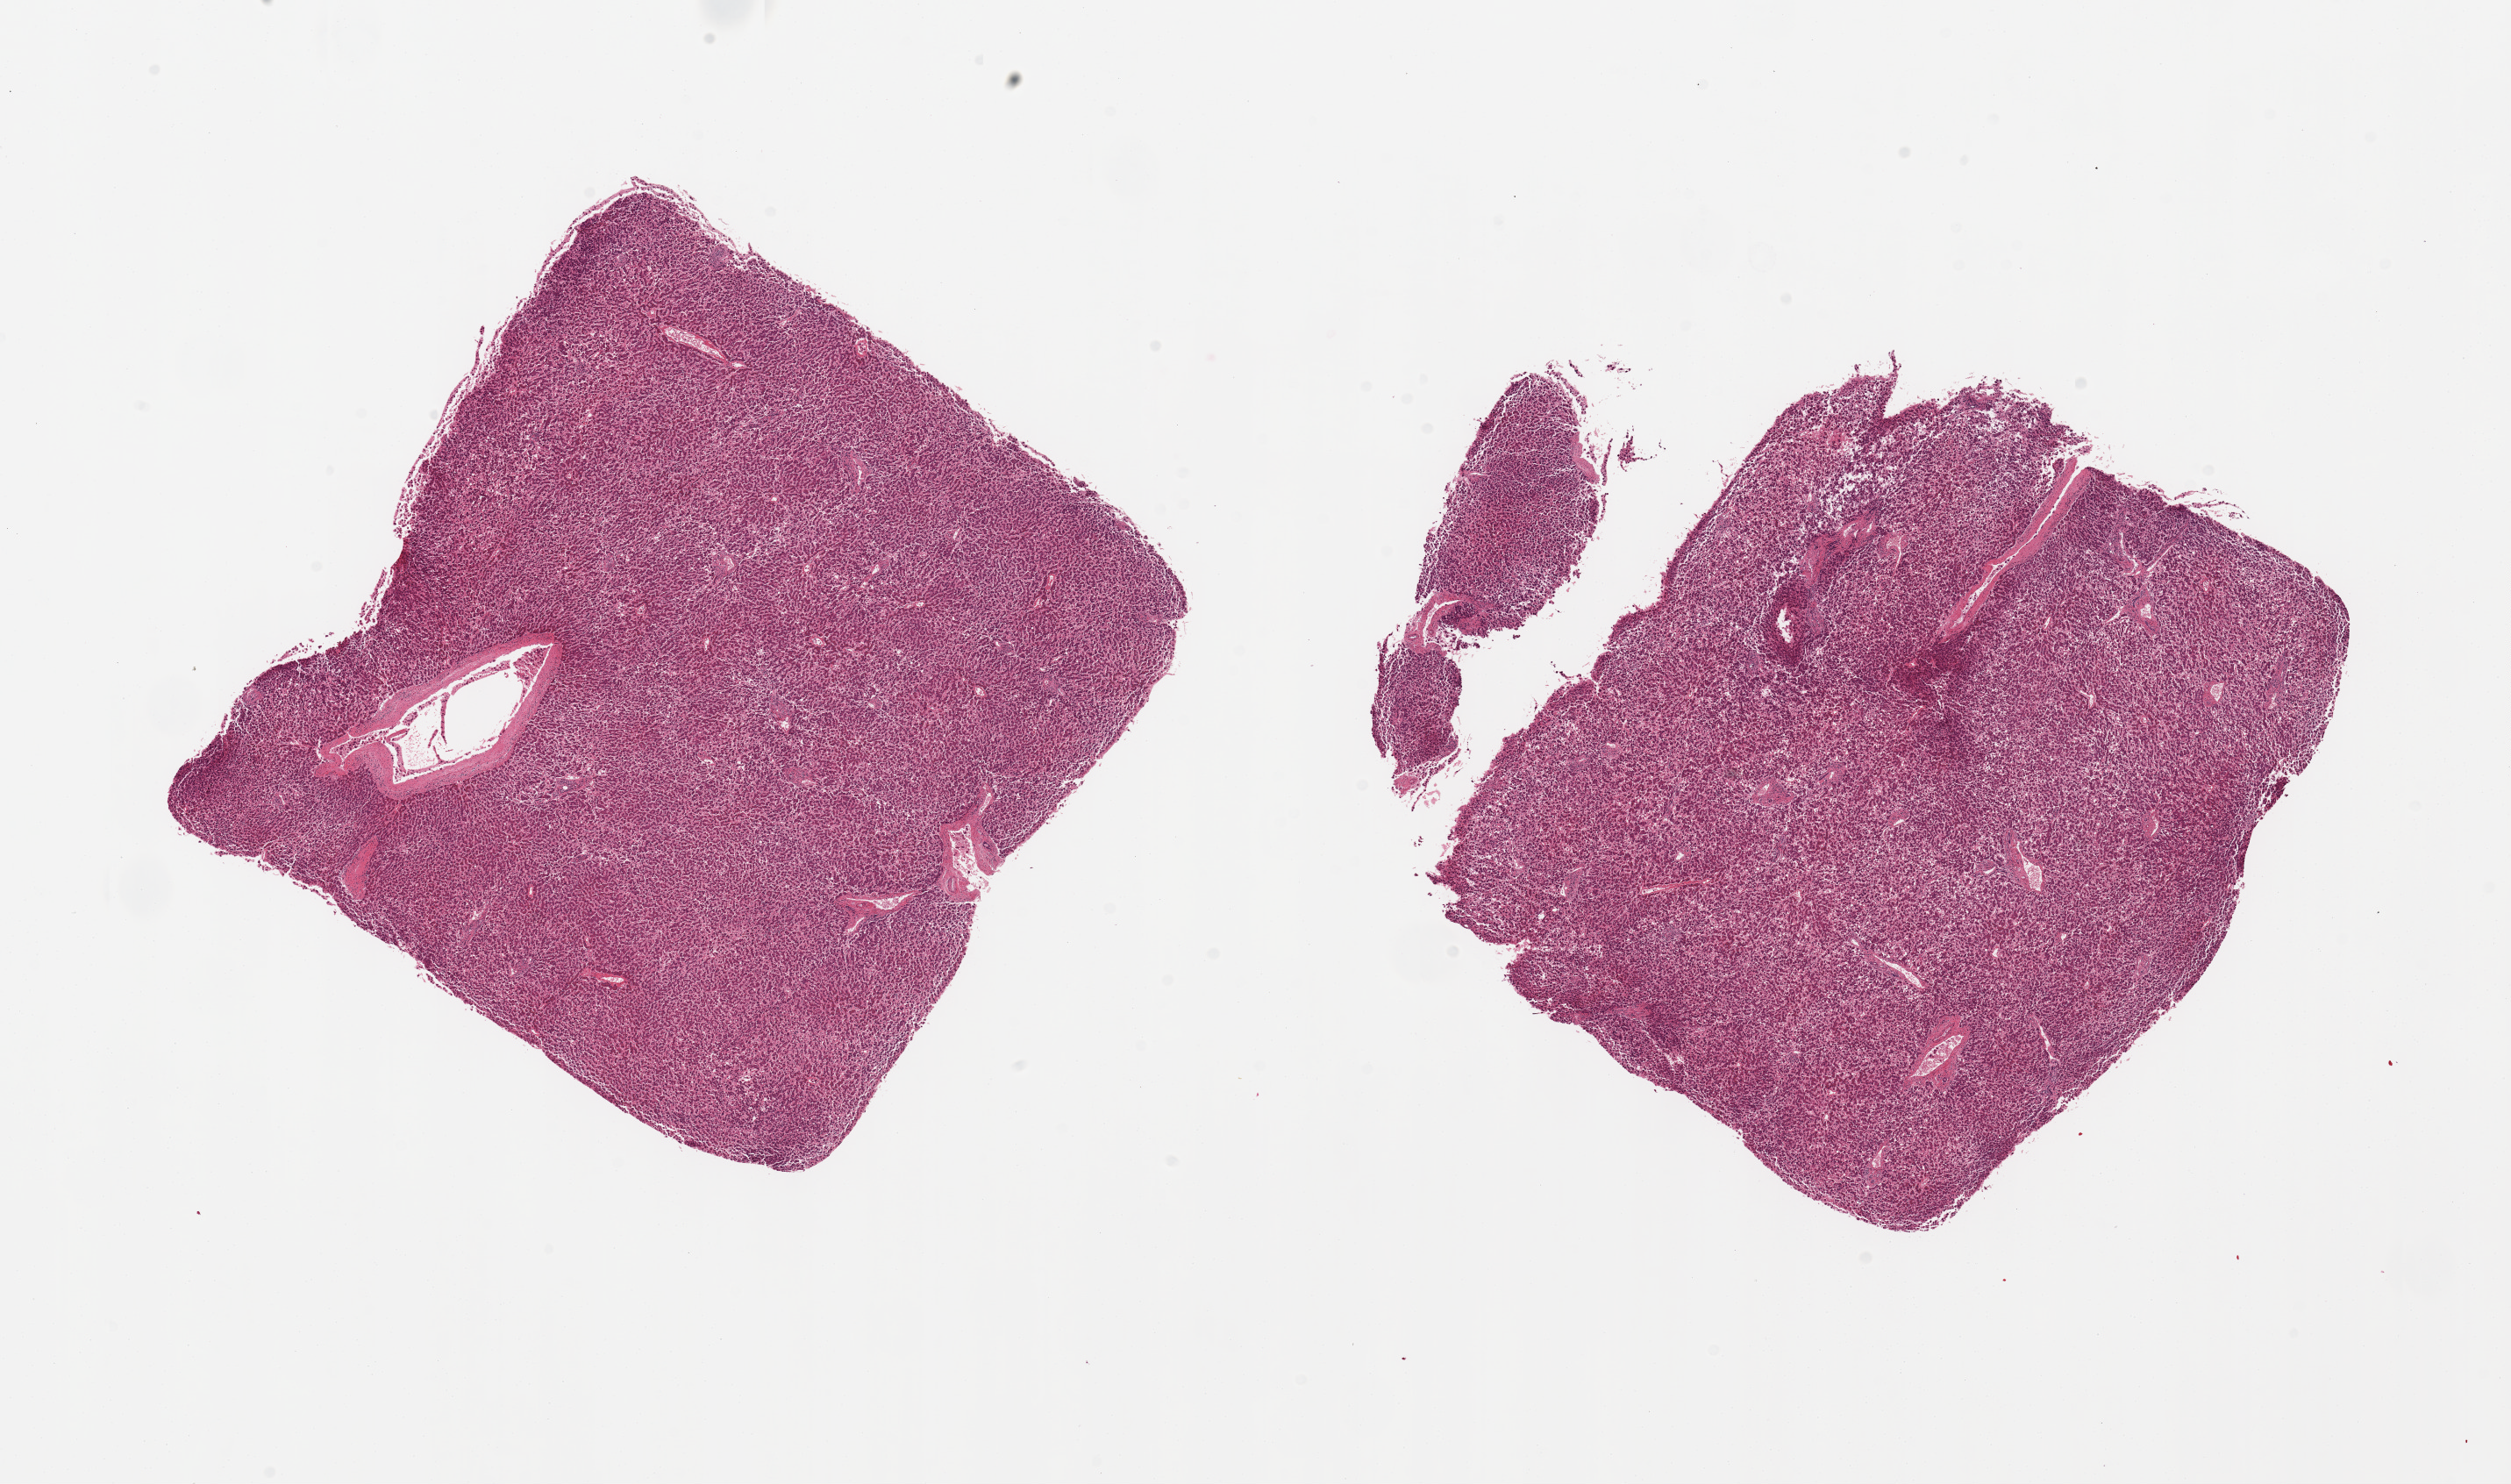
Whole-slide image, haematoxylin and eosin stain, brightfield, shown as a low-resolution overview of the whole scanned area (about 22.6 x 13.4 mm), PAXgene-fixed, paraffin-embedded tissue, target tissue: liver, tissue donor sample. Donor: male.
Review note (as recorded): 2 pieces.